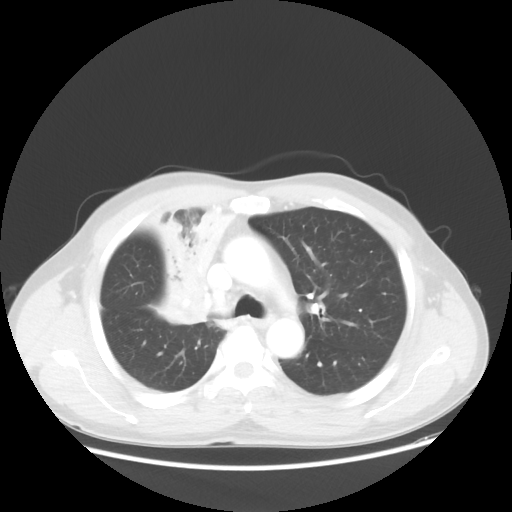
Chest CT, one axial slice; slice 37 of 56 in the series (ordered by position); reconstruction kernel STANDARD; lung window (W 1500 / L -600 HU); 5 mm slice thickness; 512 × 512 image matrix. Patient: male, 60 years. From the clinical record (not read from this slice): clinical TNM (as recorded): T2a N1 M0.
Outlined on this slice (bounding box drawn by a radiologist):
- lung tumour (recorded histology: squamous cell carcinoma): bounding box (x1, y1, x2, y2) in pixels: (134, 192, 243, 324)